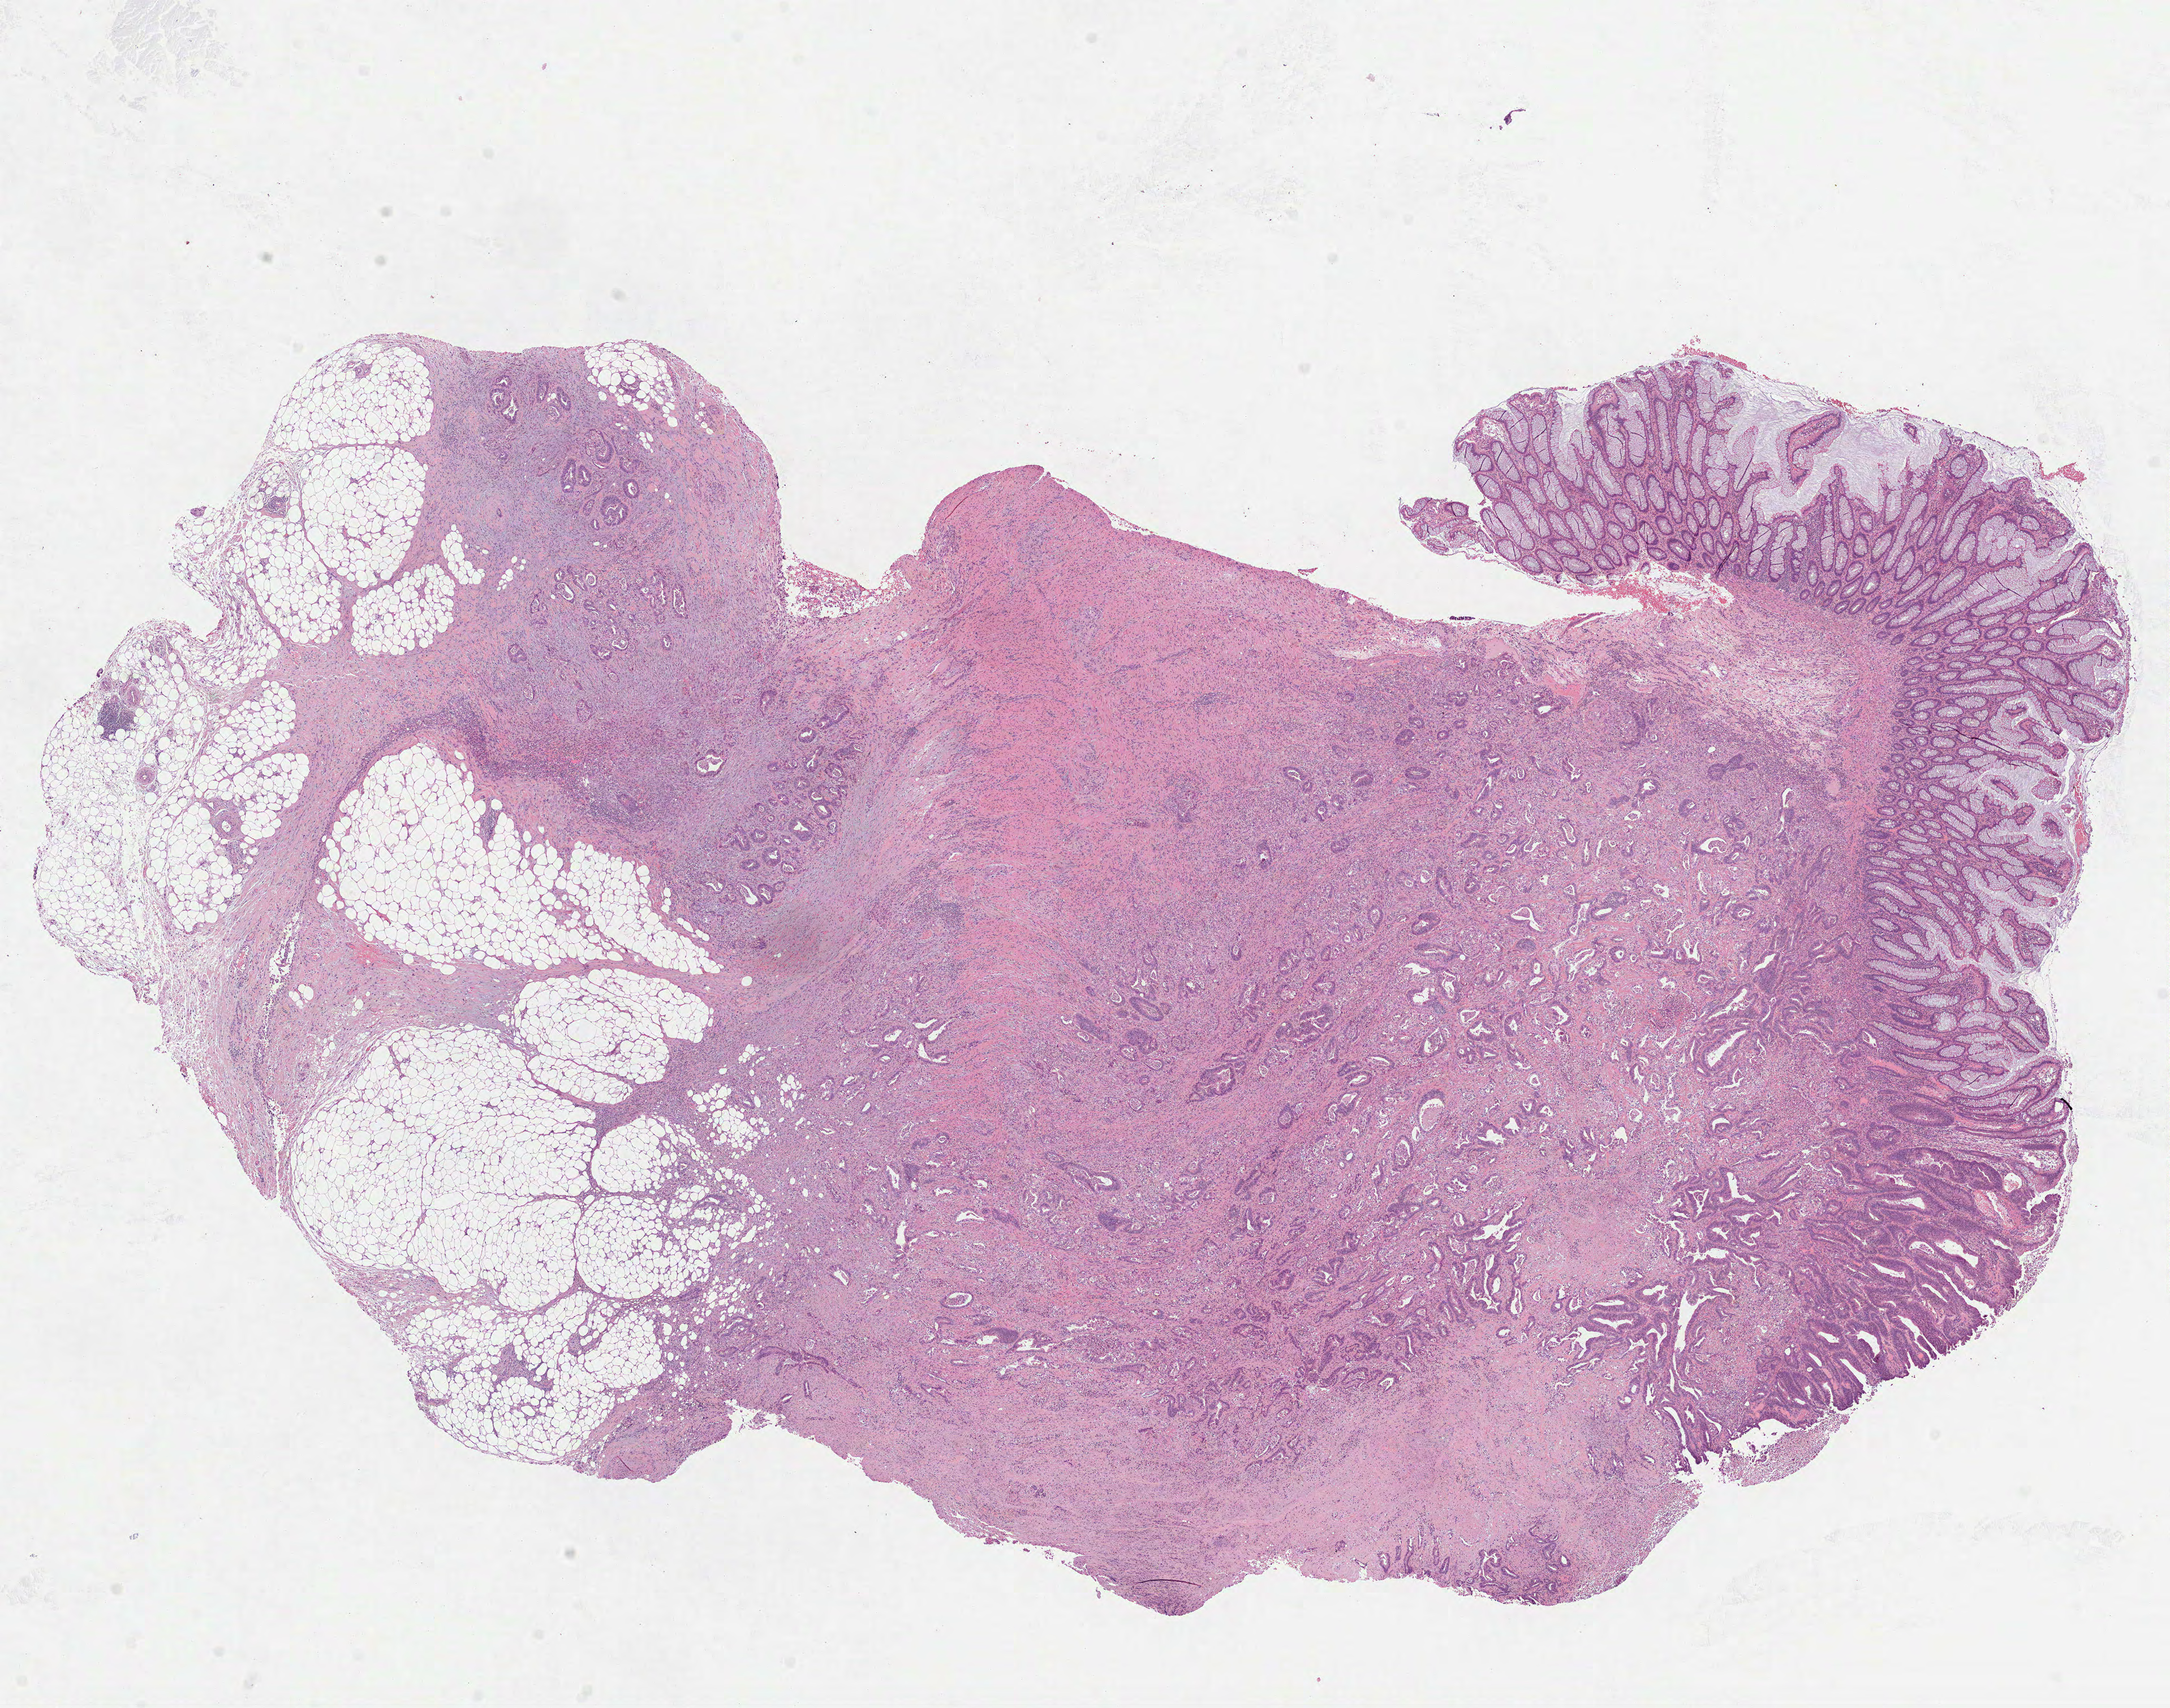
Hematoxylin and eosin (H&E) stained whole-slide image — shown as a low-resolution overview of the whole scanned area (about 15.5 x 12.2 mm), FFPE section, rectum, primary tumour sample. Male patient; age at initial diagnosis 60 years.
Diagnosis: Adenocarcinoma, NOS (rectosigmoid junction).